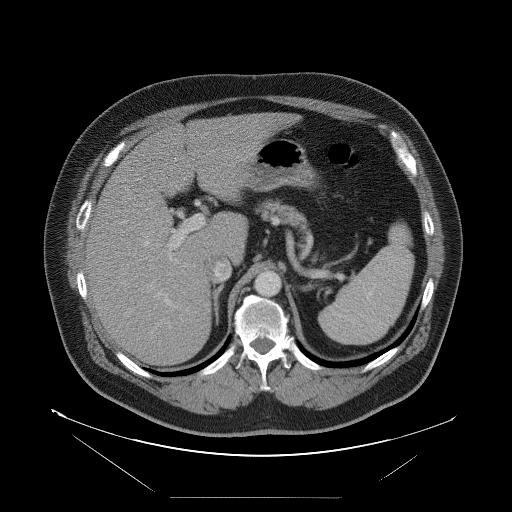
Contrast-enhanced abdominal CT, one axial slice. Slice 62 of 114 in the series (ordered by position). Intravenous contrast given. Soft-tissue window (W 400 / L 40 HU). 512 × 512 image matrix, field of view 500 × 500 mm. Male patient, age 61 years. From the clinical record (not read from this slice): diagnosis: colorectal cancer liver metastases, imaged before liver resection; multiple liver metastases: no; largest metastasis: 6.5 cm; disease in both lobes: yes.
Outlined on this slice (expert manual segmentation):
- hepatic veins: box from (x=144, y=236) to (x=150, y=247) px
- liver: (x=86, y=113)–(x=288, y=367)
- planned liver remnant (the part of the liver to remain after resection): (x=145, y=113)–(x=287, y=256)
- portal vein (with intrahepatic branches): (x=155, y=214)–(x=204, y=302)